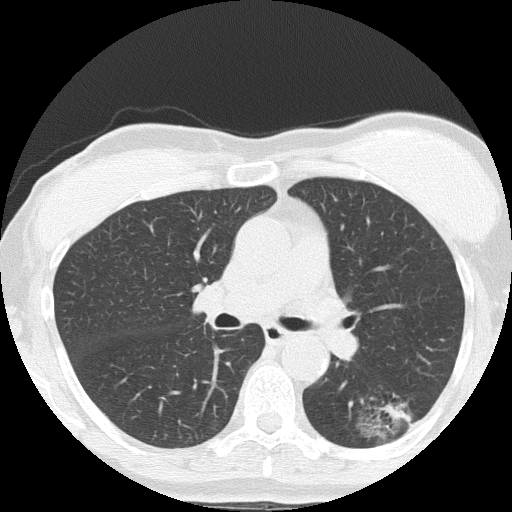
Low-dose screening chest CT, one axial slice; position 91 of 152 along the scan axis; reconstruction kernel FC51; lung window (W 1500 / L -600 HU); 2 mm slice thickness; 512 × 512 image matrix, field of view 308 × 308 mm.
Outlined on this slice (expert manual segmentation):
- lesion 1 (tumor, lower lobe of left lung): box from (x=384, y=400) to (x=407, y=421) px